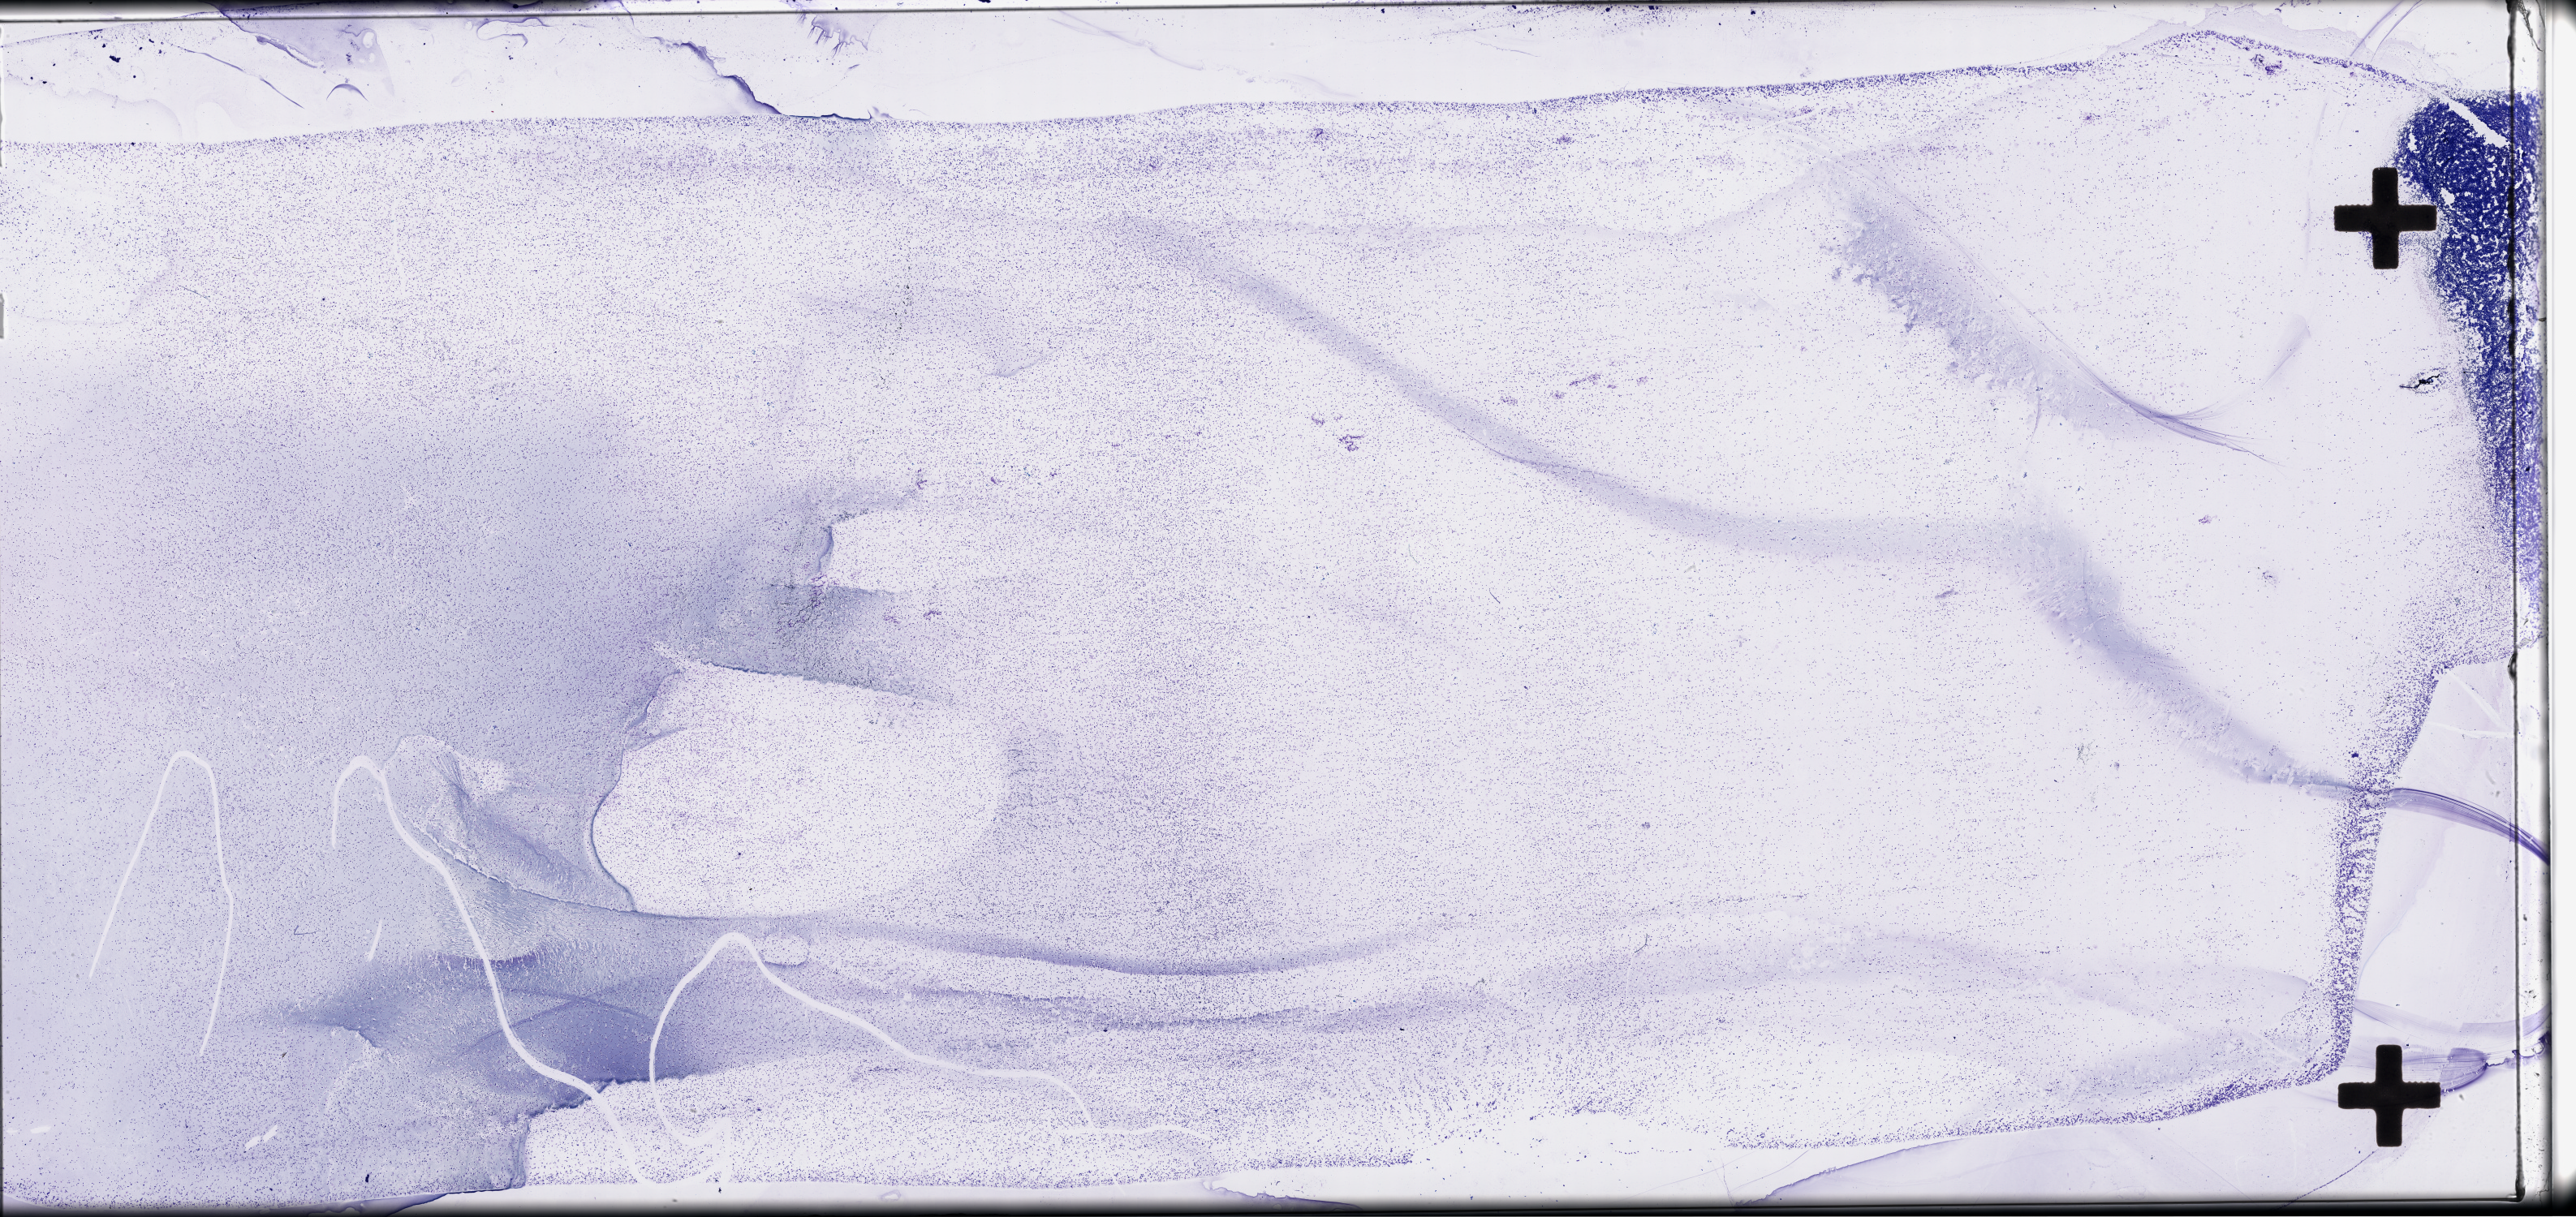
Hematoxylin and eosin (H&E) stained whole-slide image, a low-resolution overview of the entire scanned area, about 51.3 x 24.2 mm (acquisition: 40x scan). Peripheral blood (leukaemic) sample. 74-year-old male patient.
FAB classification: M2. Diagnosis: Acute Myeloid Leukemia.